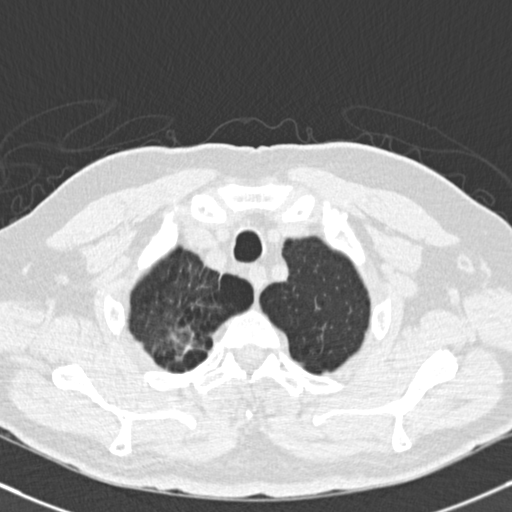
Low-dose screening chest CT, one axial slice. Slice 145 of 165 in the series (ordered by position). Lung window (W 1500 / L -600 HU). 512 × 512 image matrix, field of view 324 × 324 mm.
Structures marked on this image (outlined manually by an expert reader):
- lesion 1 (tumor, upper lobe of right lung): box from (x=169, y=327) to (x=195, y=360) px